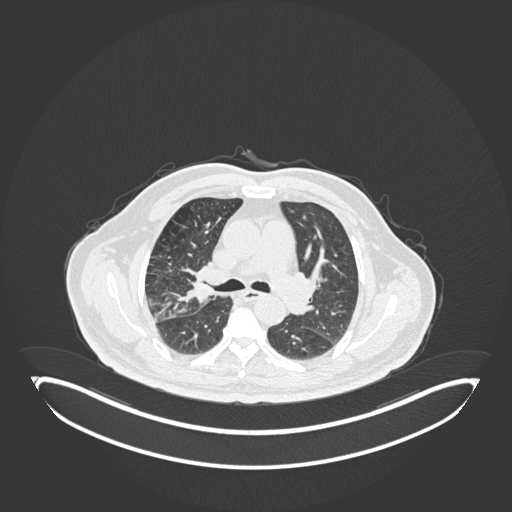
Chest CT, one axial slice; slice 110 of 247 in the series (ordered by position); reconstruction kernel B30f; 120 kVp; lung window (W 1500 / L -600 HU); 512 × 512 image matrix, field of view 500 × 500 mm. Patient: male, 72 years. Case-level facts recorded for this patient, not image findings: clinical TNM (as recorded): T1c N0 M0; histopathological grade: G2.
Outlined on this slice (bounding box drawn by a radiologist):
- lung tumour (recorded histology: squamous cell carcinoma): bounding box <176,259,208,304> (left, top, right, bottom; pixels)